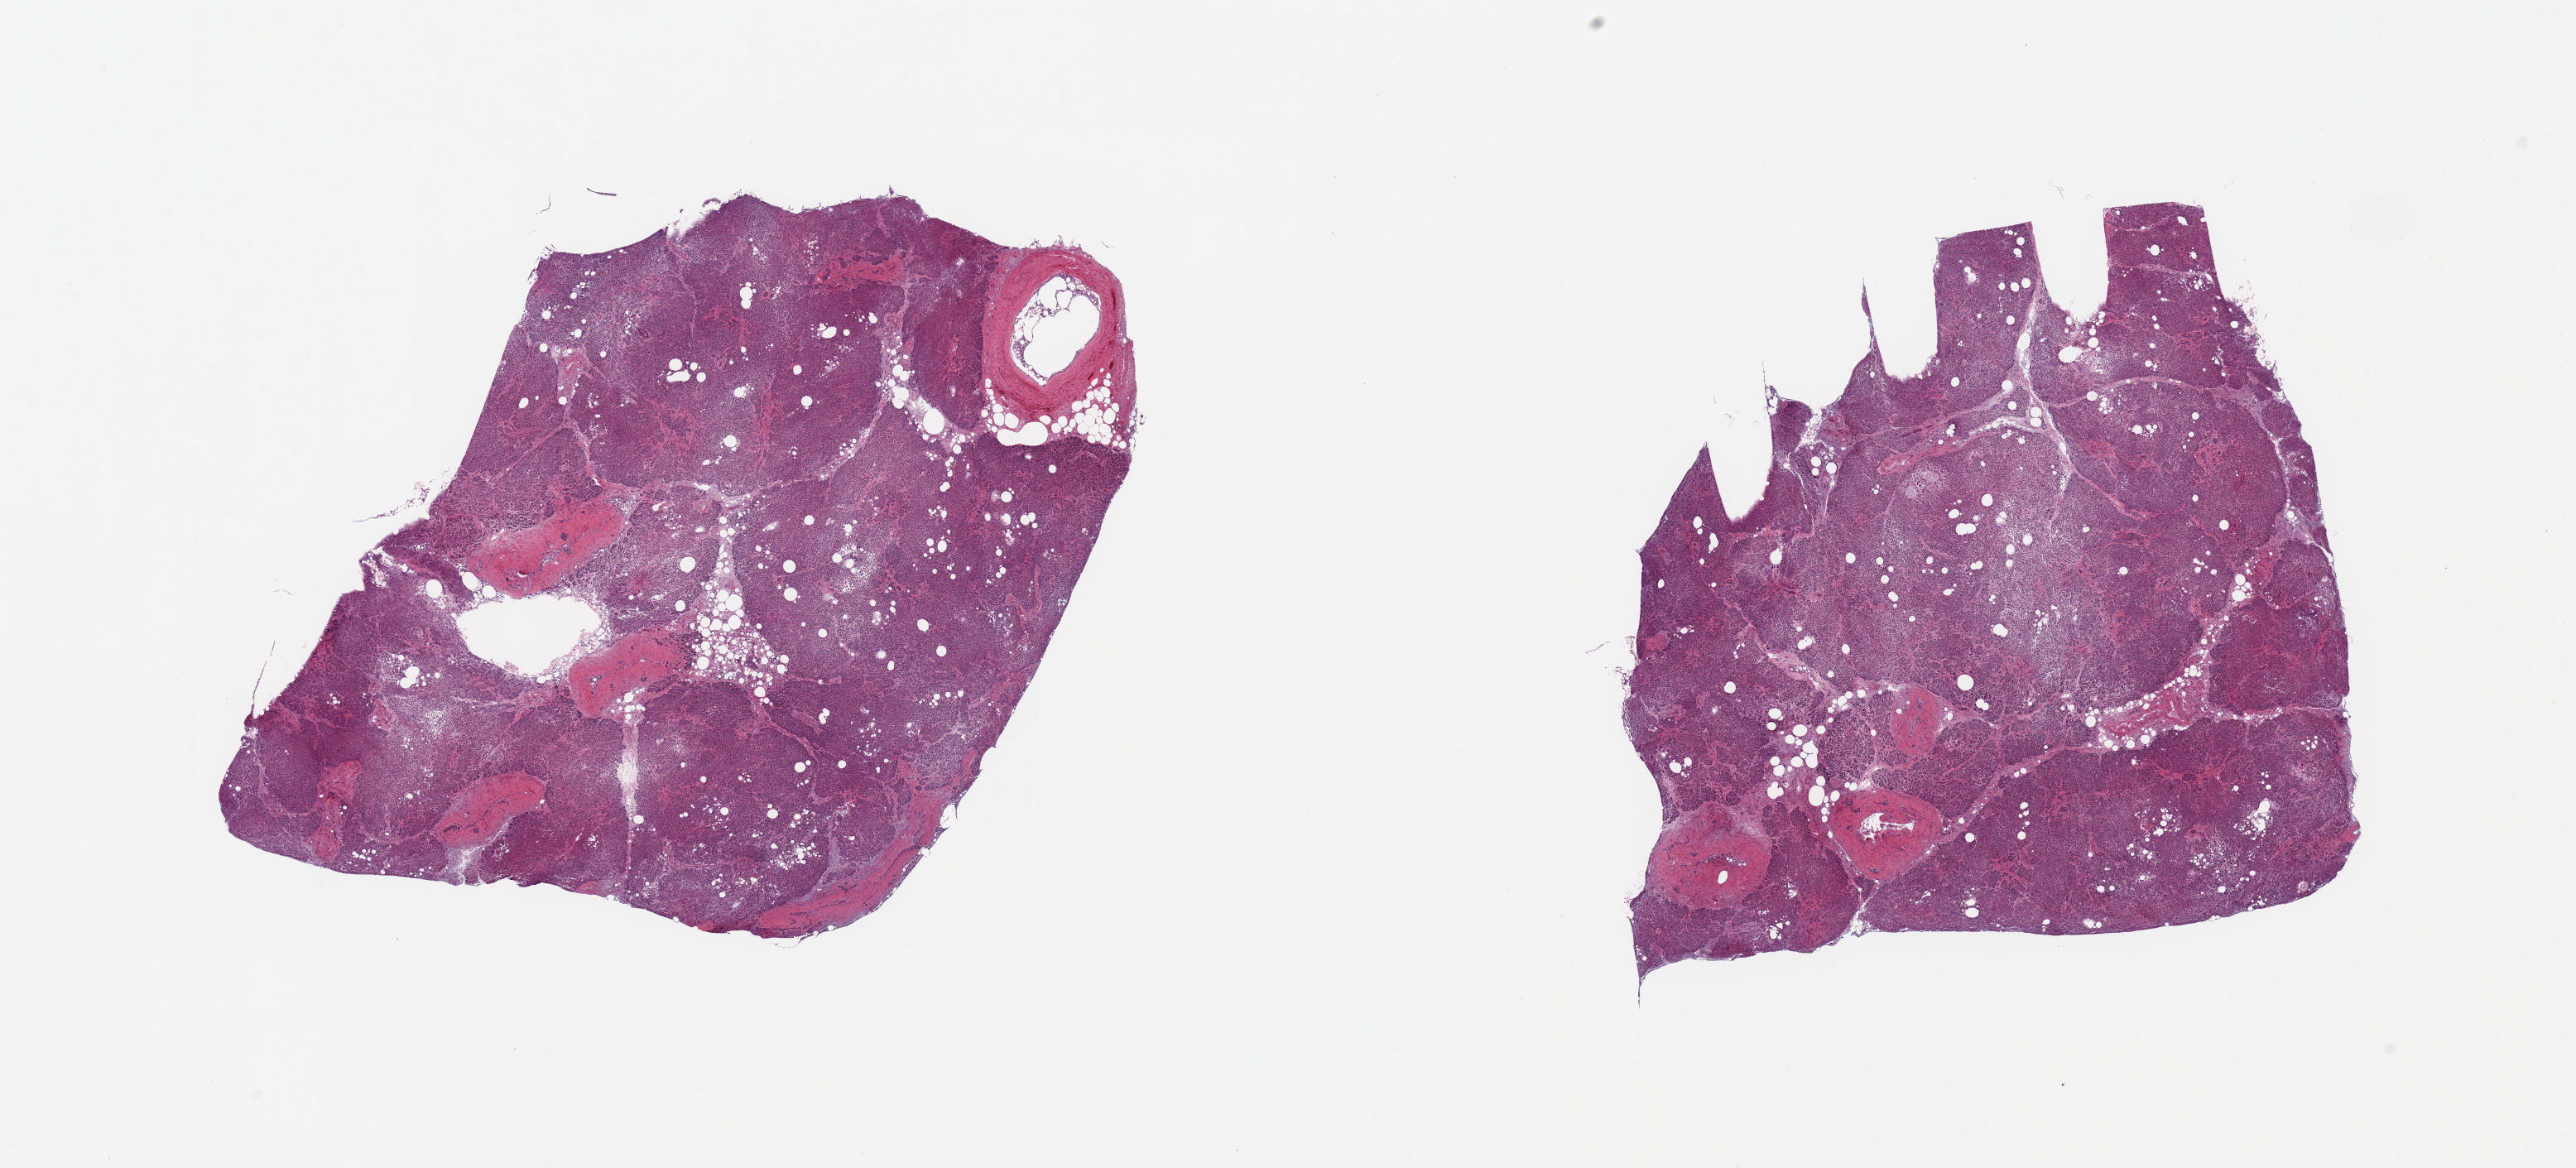
Whole-slide image, haematoxylin and eosin stain, brightfield, a low-resolution overview of the entire scanned area, about 24.6 x 11.2 mm. PAXgene-fixed, paraffin-embedded tissue. Target tissue: pancreas. Tissue donor sample.
- review note (as recorded): 2 pieces